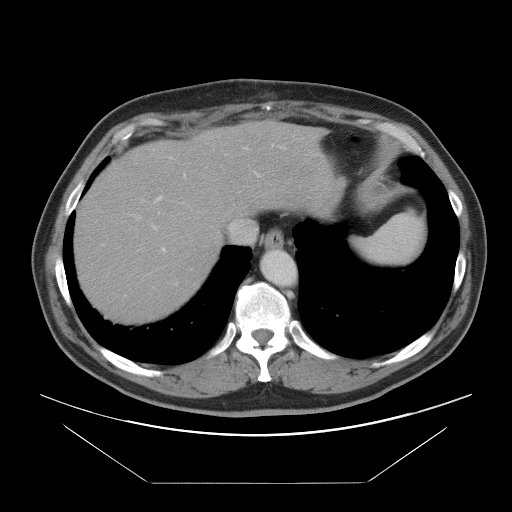
Contrast-enhanced abdominal CT, one axial slice; slice 77 of 97 in the series (ordered by position); soft-tissue window (W 400 / L 40 HU); 5 mm slice thickness; 512 × 512 image matrix, field of view 442 × 442 mm. Male patient, age 62 years. Case-level facts recorded for this patient, not image findings: diagnosis: colorectal cancer liver metastases, imaged before liver resection; multiple liver metastases: no; largest metastasis: 7 cm; disease in both lobes: yes.
Outlined on this slice (outlined manually by an expert reader):
- hepatic veins: bounding box (x1, y1, x2, y2) in pixels: (229, 220, 247, 243)
- liver: (74, 124, 334, 320)
- planned liver remnant (the part of the liver to remain after resection): (74, 172, 226, 320)
- portal vein (with intrahepatic branches): (125, 144, 285, 296)